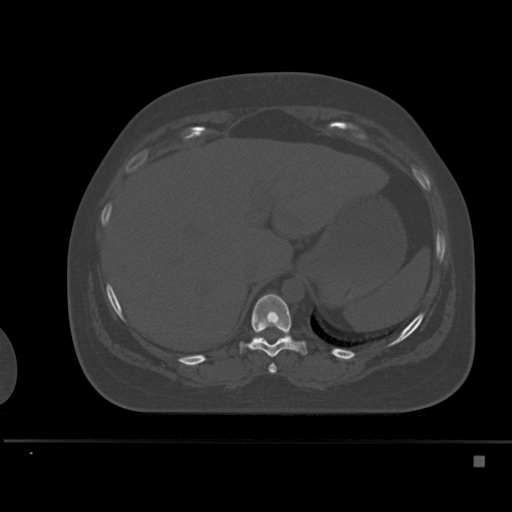
CT including the spine, one axial slice; position 247 of 495 along the scan axis; bone window (W 1800 / L 400 HU); 1.5 mm slice thickness; 512 × 512 image matrix. Female patient, age 33 years. From the clinical record (not read from this slice): primary cancer: breast.
Annotated regions visible in this slice (semi-automatically segmented with operator editing):
- T10 vertebra: box from (x=240, y=294) to (x=307, y=358) px
- T9 vertebra: (x=268, y=364)–(x=277, y=373)